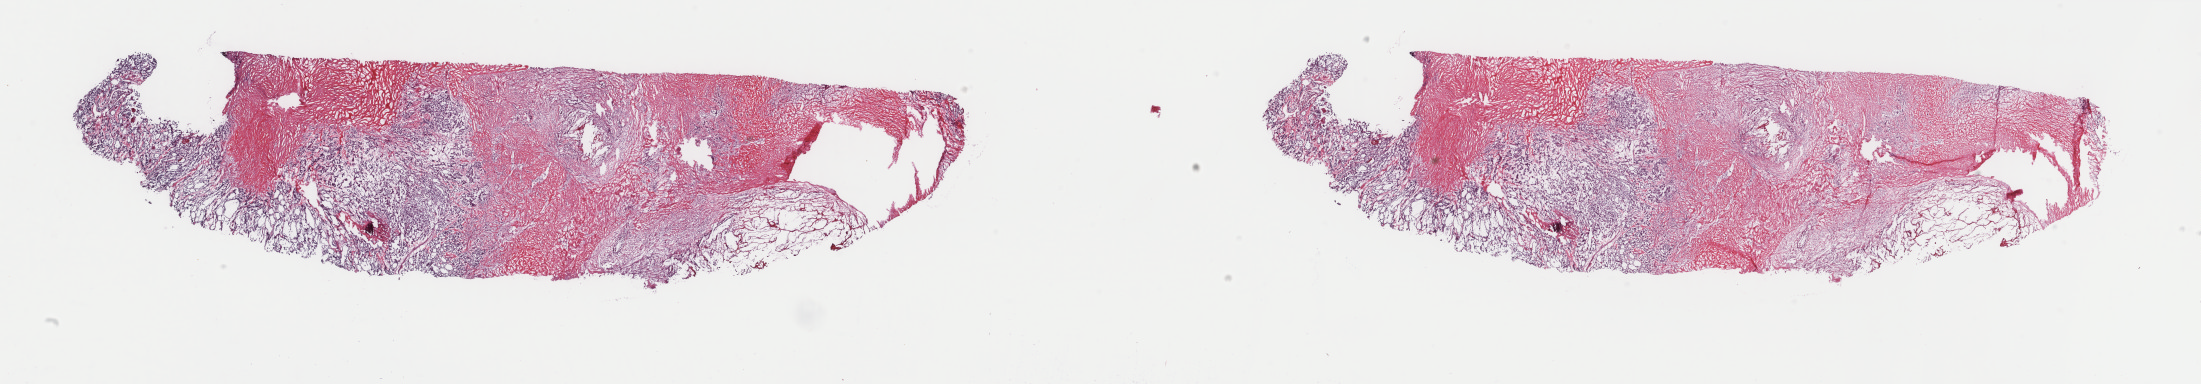
Whole-slide histology image, H&E-stained, low-resolution overview of the scanned area, about 34.9 x 6.1 mm (slide scanned at 40x); frozen section from the top of the tissue portion; primary tumour sample from the thyroid. Female, age 51 years at initial diagnosis. Slide review estimates, as recorded: tumour cells 30%, tumour nuclei 90%, normal cells 10%, stromal cells 60%, necrosis 0%. Infiltration values recorded for this section: lymphocyte infiltration 1%, monocyte infiltration 1%, neutrophil infiltration 0%.
- AJCC pathologic stage: III (7th edition)
- diagnosis: Papillary adenocarcinoma, NOS (thyroid gland)